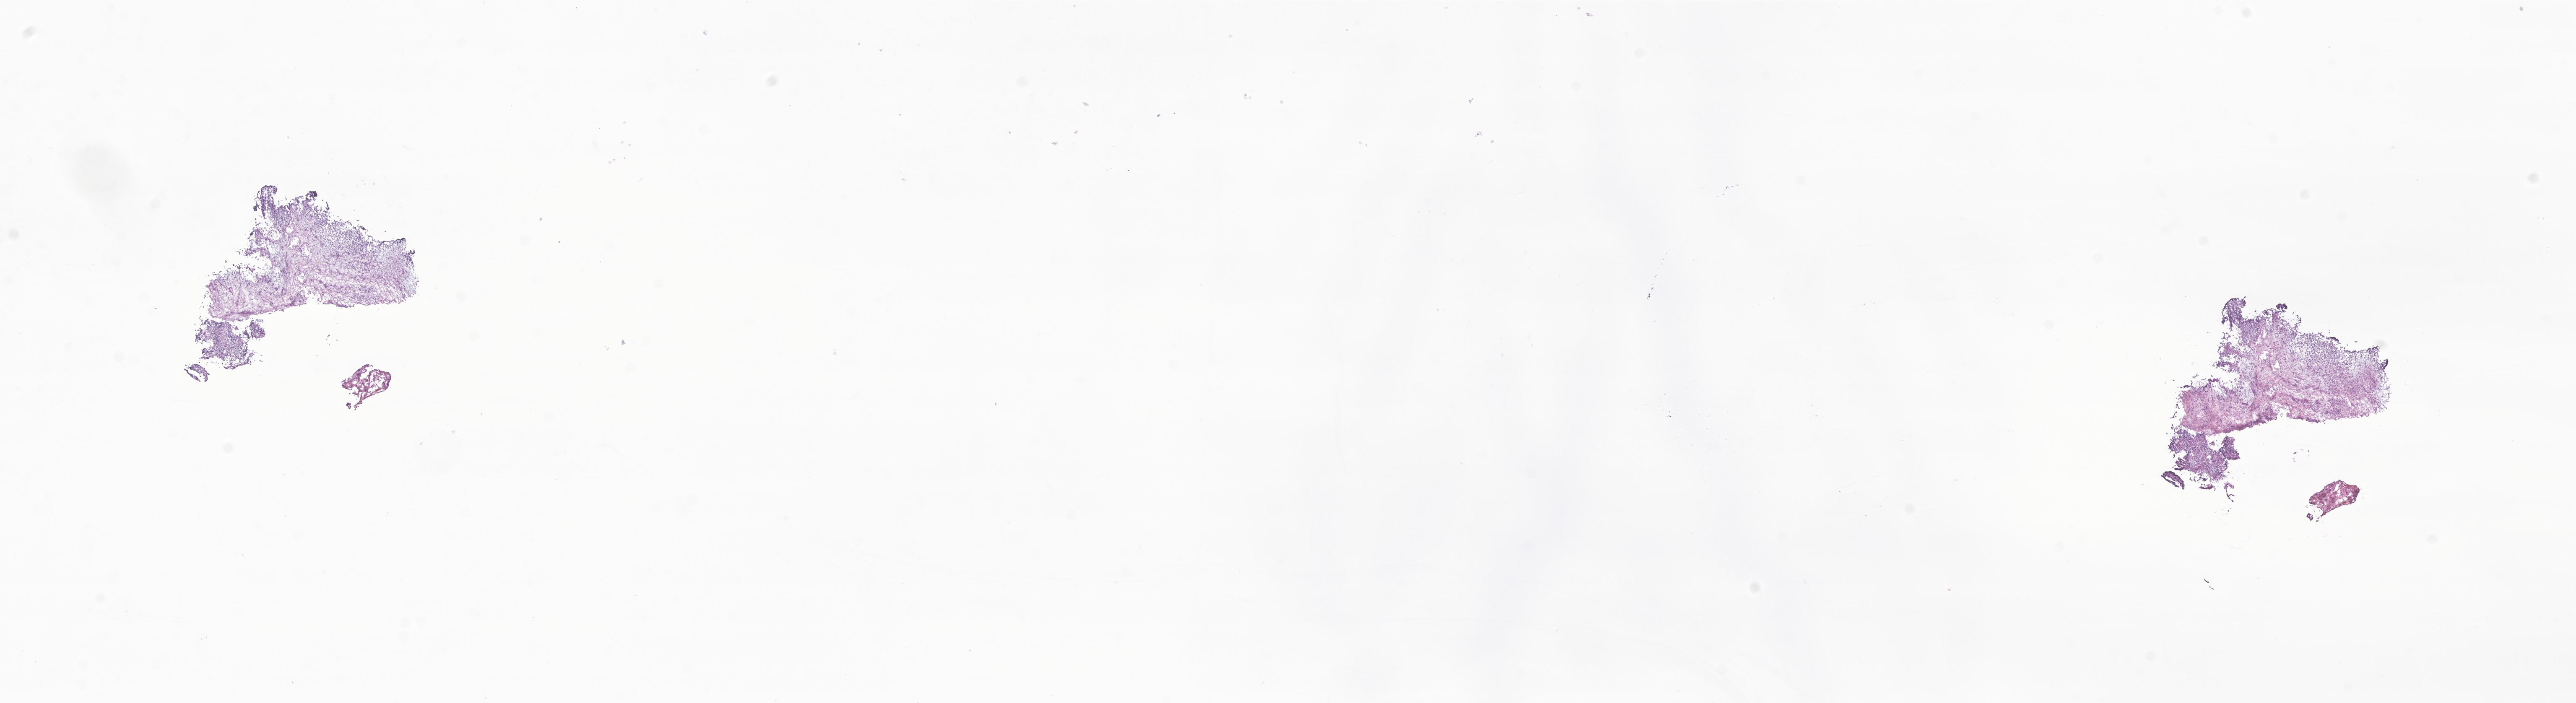
H&E whole-slide image of tumor tissue from the orbit — a low-resolution overview of the entire scanned area, about 25.9 x 7.1 mm, cryosection (OCT / tissue freezing medium). Patient: female, age 396 days (about 1.1 years).
Diagnosis (ICD-O-3 morphology term): Embryonal rhabdomyosarcoma, NOS.